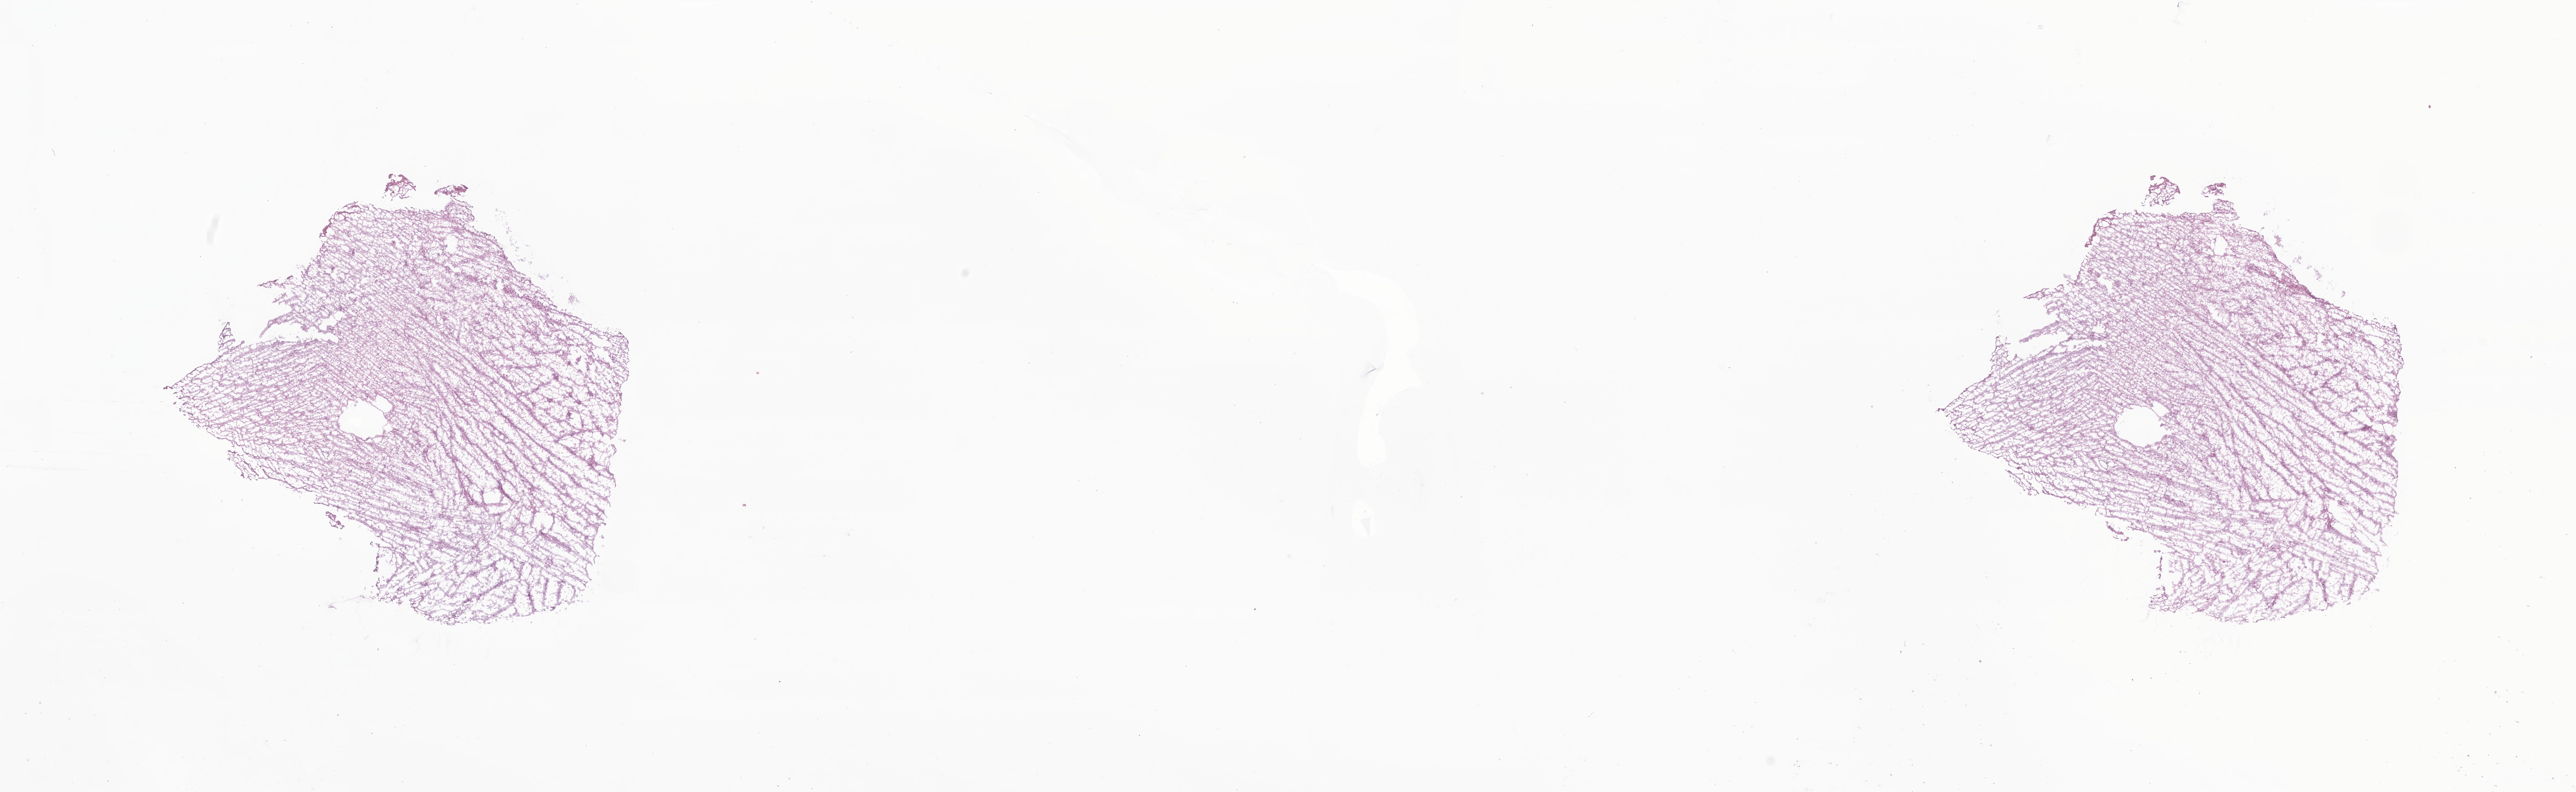
Hematoxylin and eosin (H&E) whole-slide image of tumor tissue from the frontal lobe, shown as a low-resolution overview of the whole scanned area (about 29.3 x 9.0 mm); frozen section (OCT-embedded). Male patient, age 253 months (21 years 1 month).
Diagnosis (ICD-O-3 morphology term): Astrocytoma, NOS.